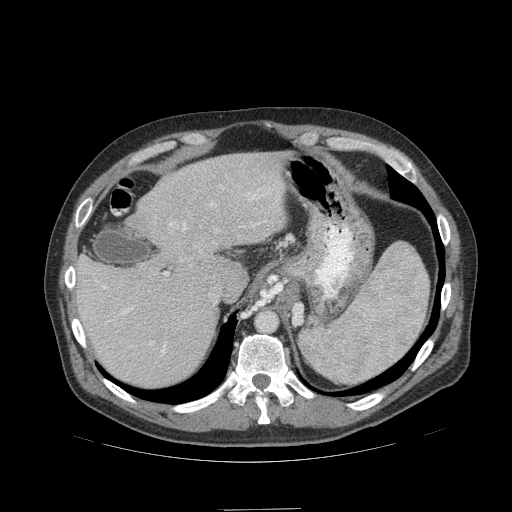
Contrast-enhanced abdominal CT (liver protocol), one axial slice. Slice 77 of 99 in the series (ordered by position). Reconstruction kernel STANDARD. 140 kVp. Soft-tissue window (W 400 / L 40 HU). 512 × 512 image matrix, field of view 440 × 440 mm. From the clinical record (not read from this slice): diagnosis: hepatocellular carcinoma (patient treated with transarterial chemoembolisation; whether this scan precedes or follows treatment is not stated here); TNM stage (as recorded): Stage-I; Child-Pugh class: A; tumour nodularity: uninodular; tumour size: 3.6 cm.
Structures marked on this image (semi-automatic segmentation, software-assisted and operator-edited):
- liver parenchyma outside the tumour (the mass and vessels are separate outlines, so this box may not span the whole liver): bounding box (x1, y1, x2, y2) in pixels: (74, 152, 286, 386)
- liver vessels: (91, 187, 279, 356)